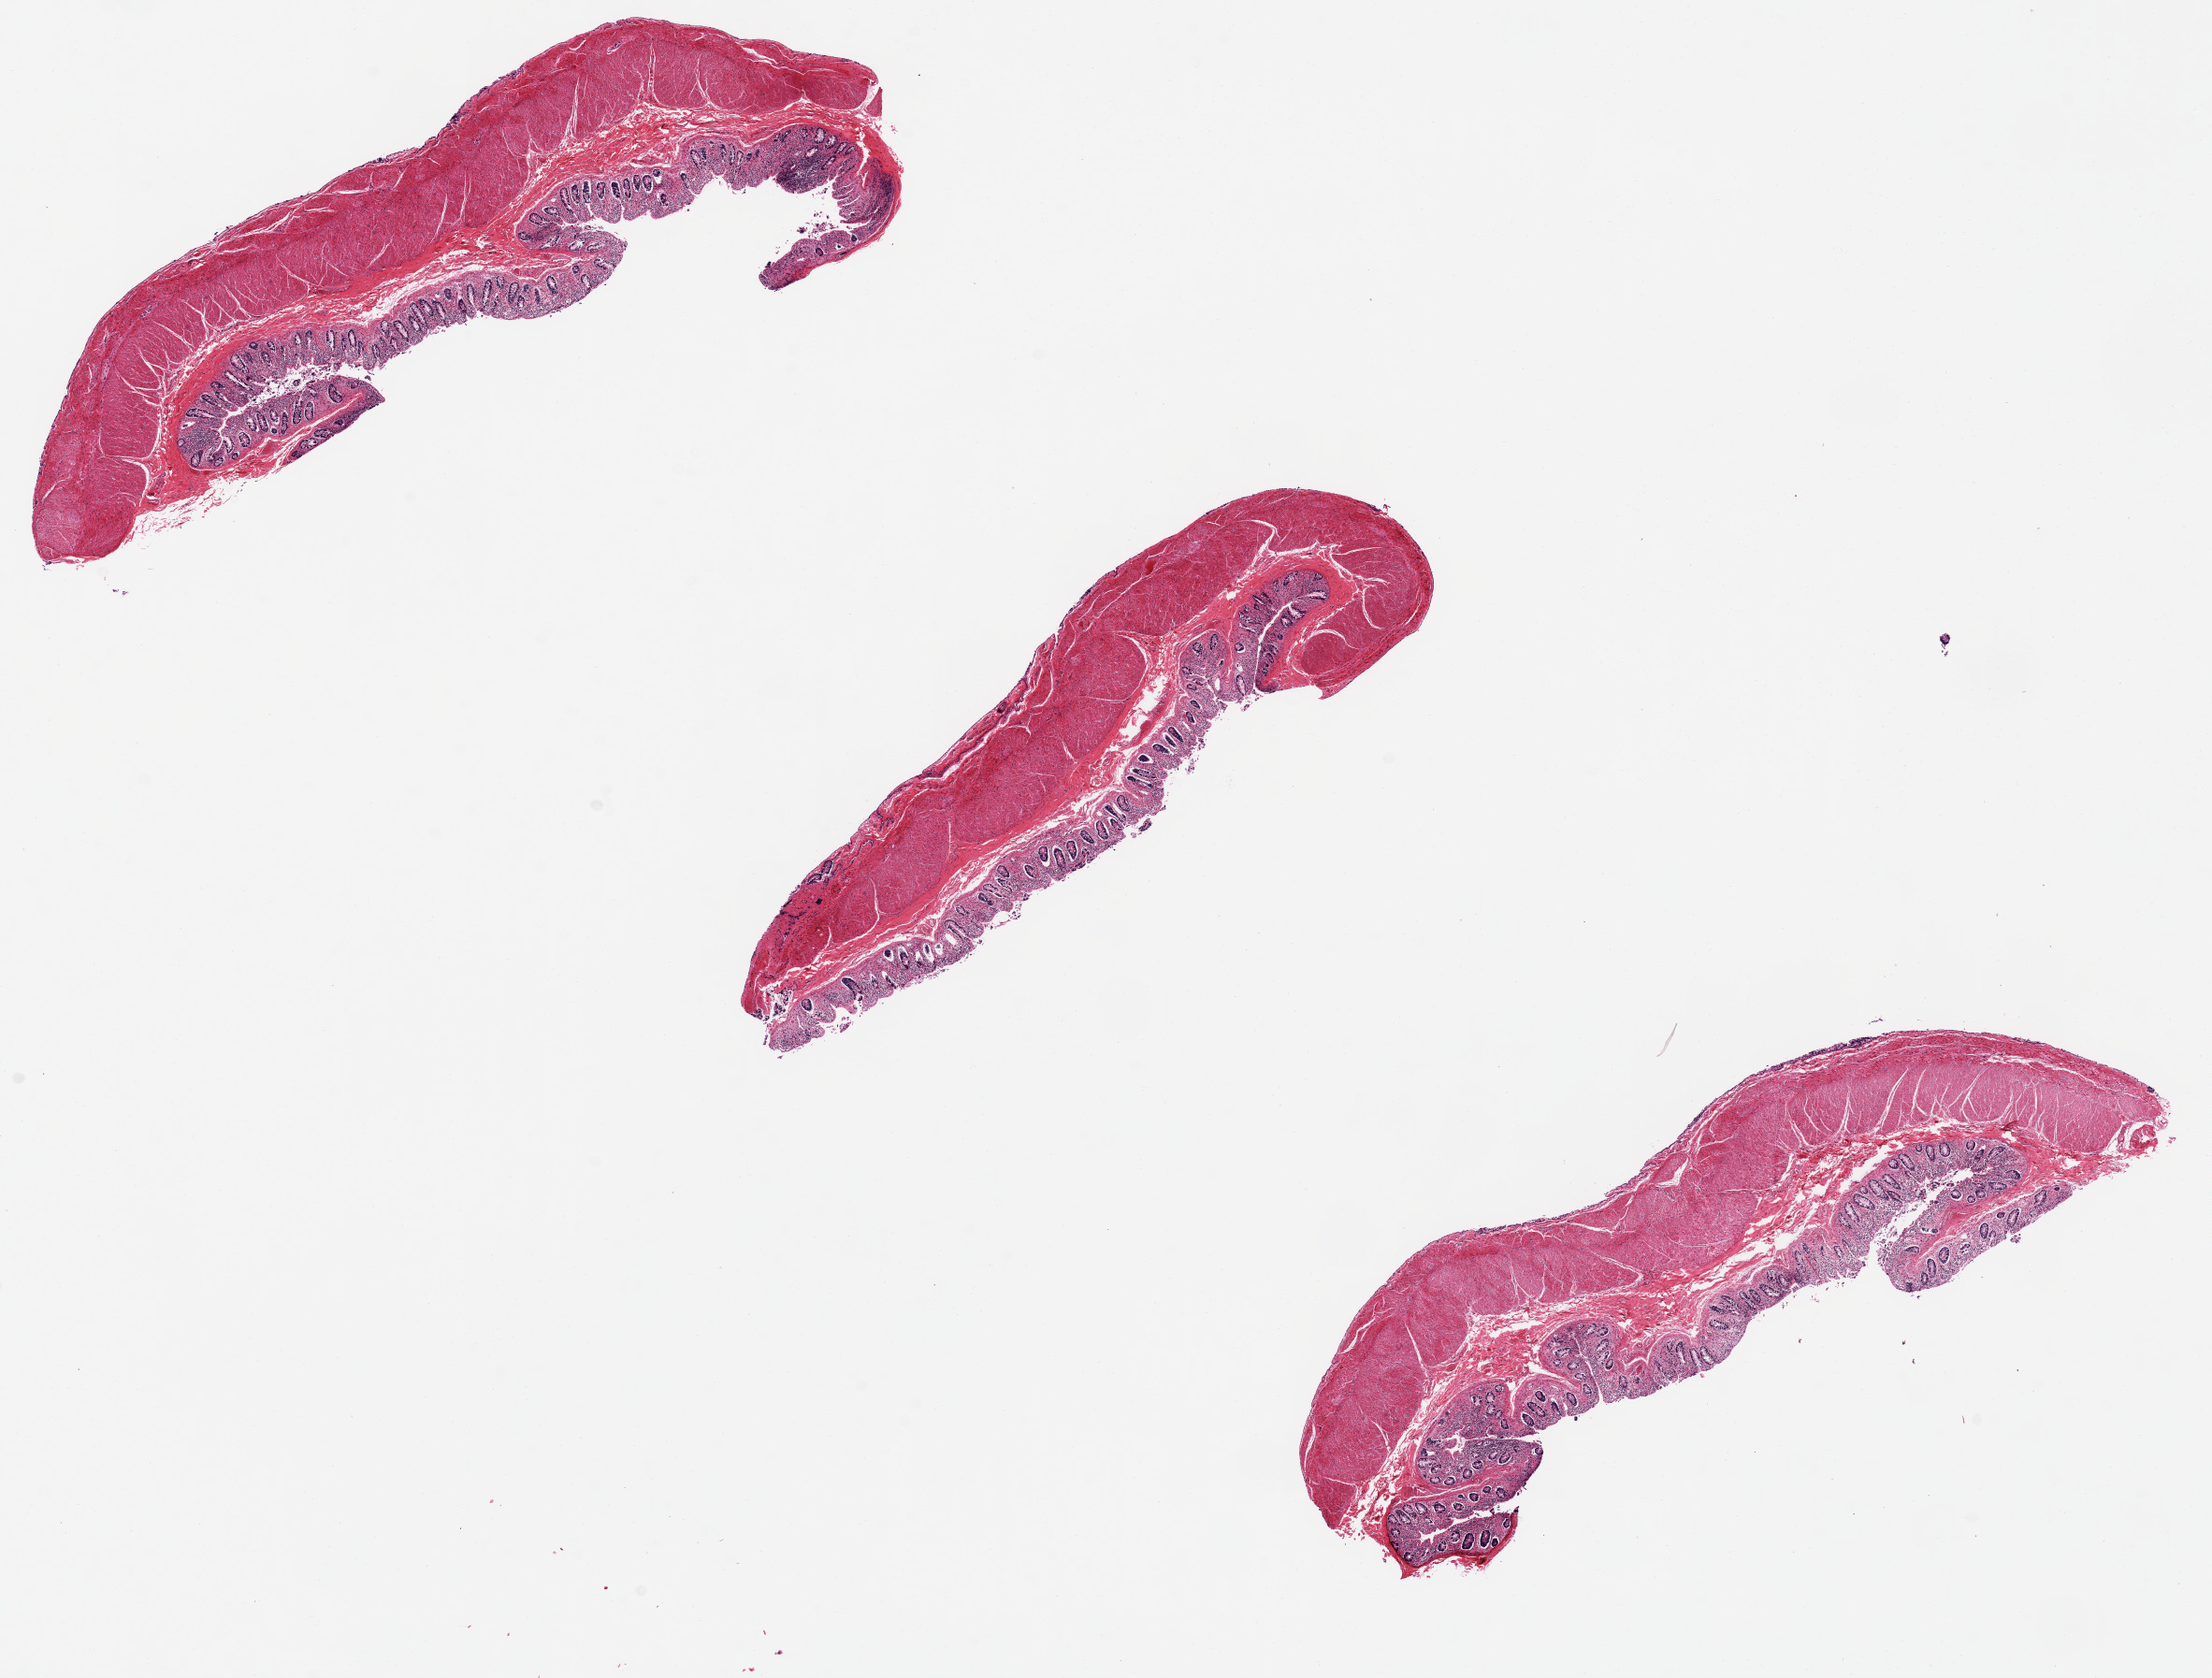
Digitized H&E-stained section, brightfield — a low-resolution overview of the entire scanned area, about 18.7 x 14.2 mm (acquisition: 20x scan), PAXgene-fixed paraffin-embedded (PFPE) section, sampled site (target tissue): transverse colon, donor tissue sample. Donor: male.
Reviewer comment on this tissue sample: 3 pieces ave 7.5x1.5mm. Mucosa ave 15-20% of specimen thickness.